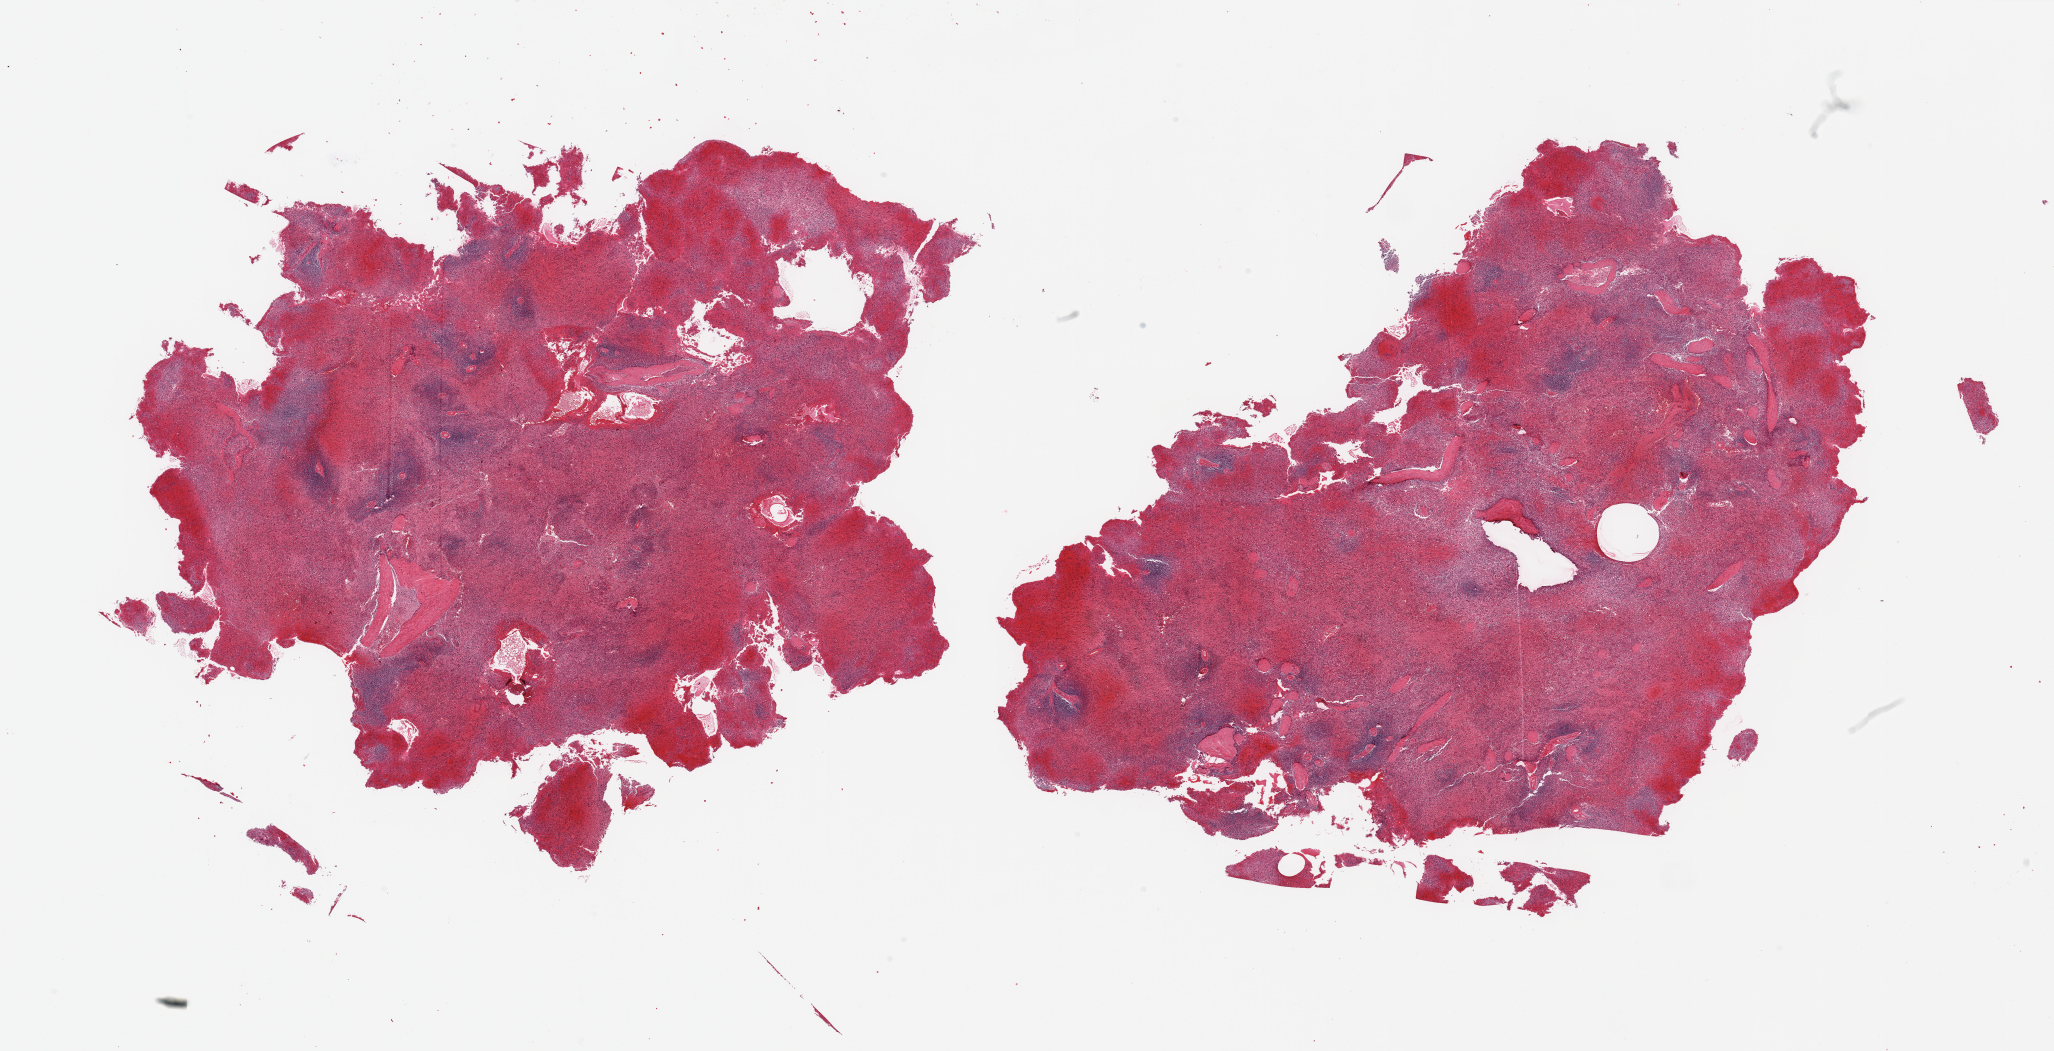
Whole-slide image, hematoxylin and eosin (H&E) stain, low-resolution overview of the scanned area, about 32.5 x 16.6 mm. PAXgene-fixed paraffin-embedded (PFPE) section. Sampled site (target tissue): spleen. Donor tissue sample. Donor sex: male.
Review note (as recorded): 2 pieces; marked congestion.